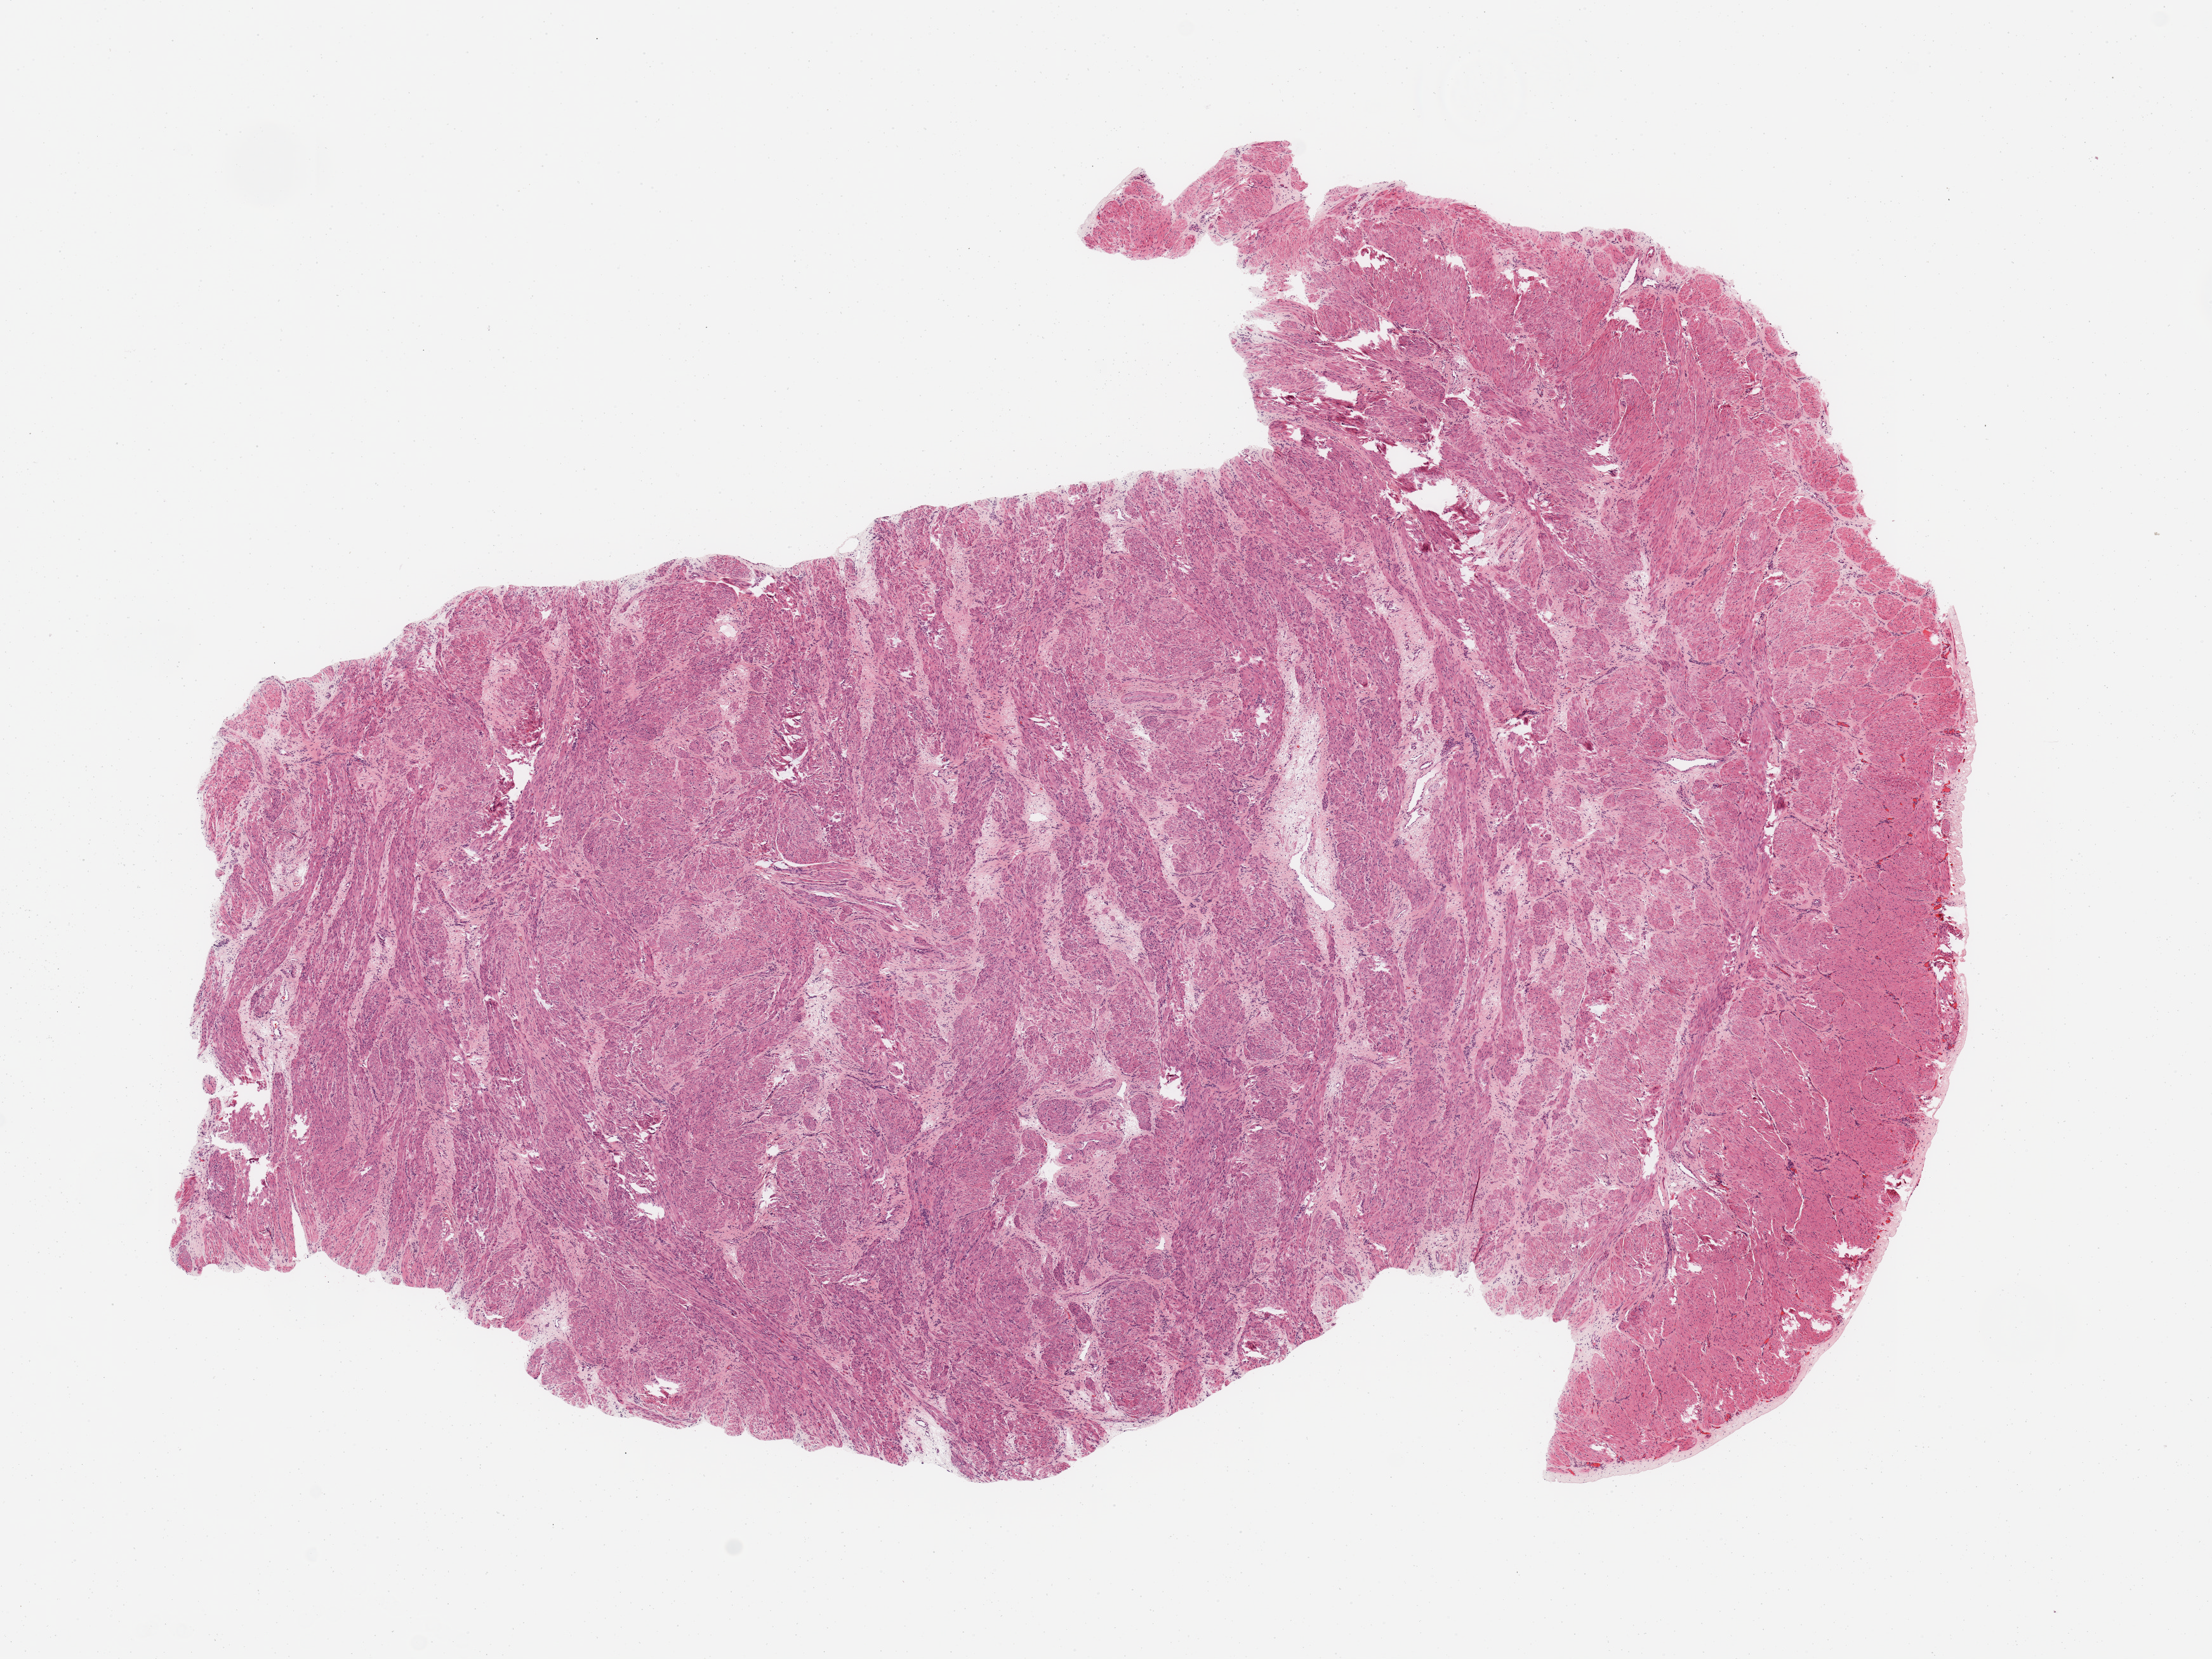
Digitized H&E-stained tissue section (whole slide) — a low-resolution overview of the entire scanned area, about 13.8 x 10.3 mm; normal (non-tumour) tissue sample, uterus. Female, 38 y/o.
This section: normal (non-tumour) tissue from the same patient. Patient diagnosis: Endometrioid adenocarcinoma, NOS.